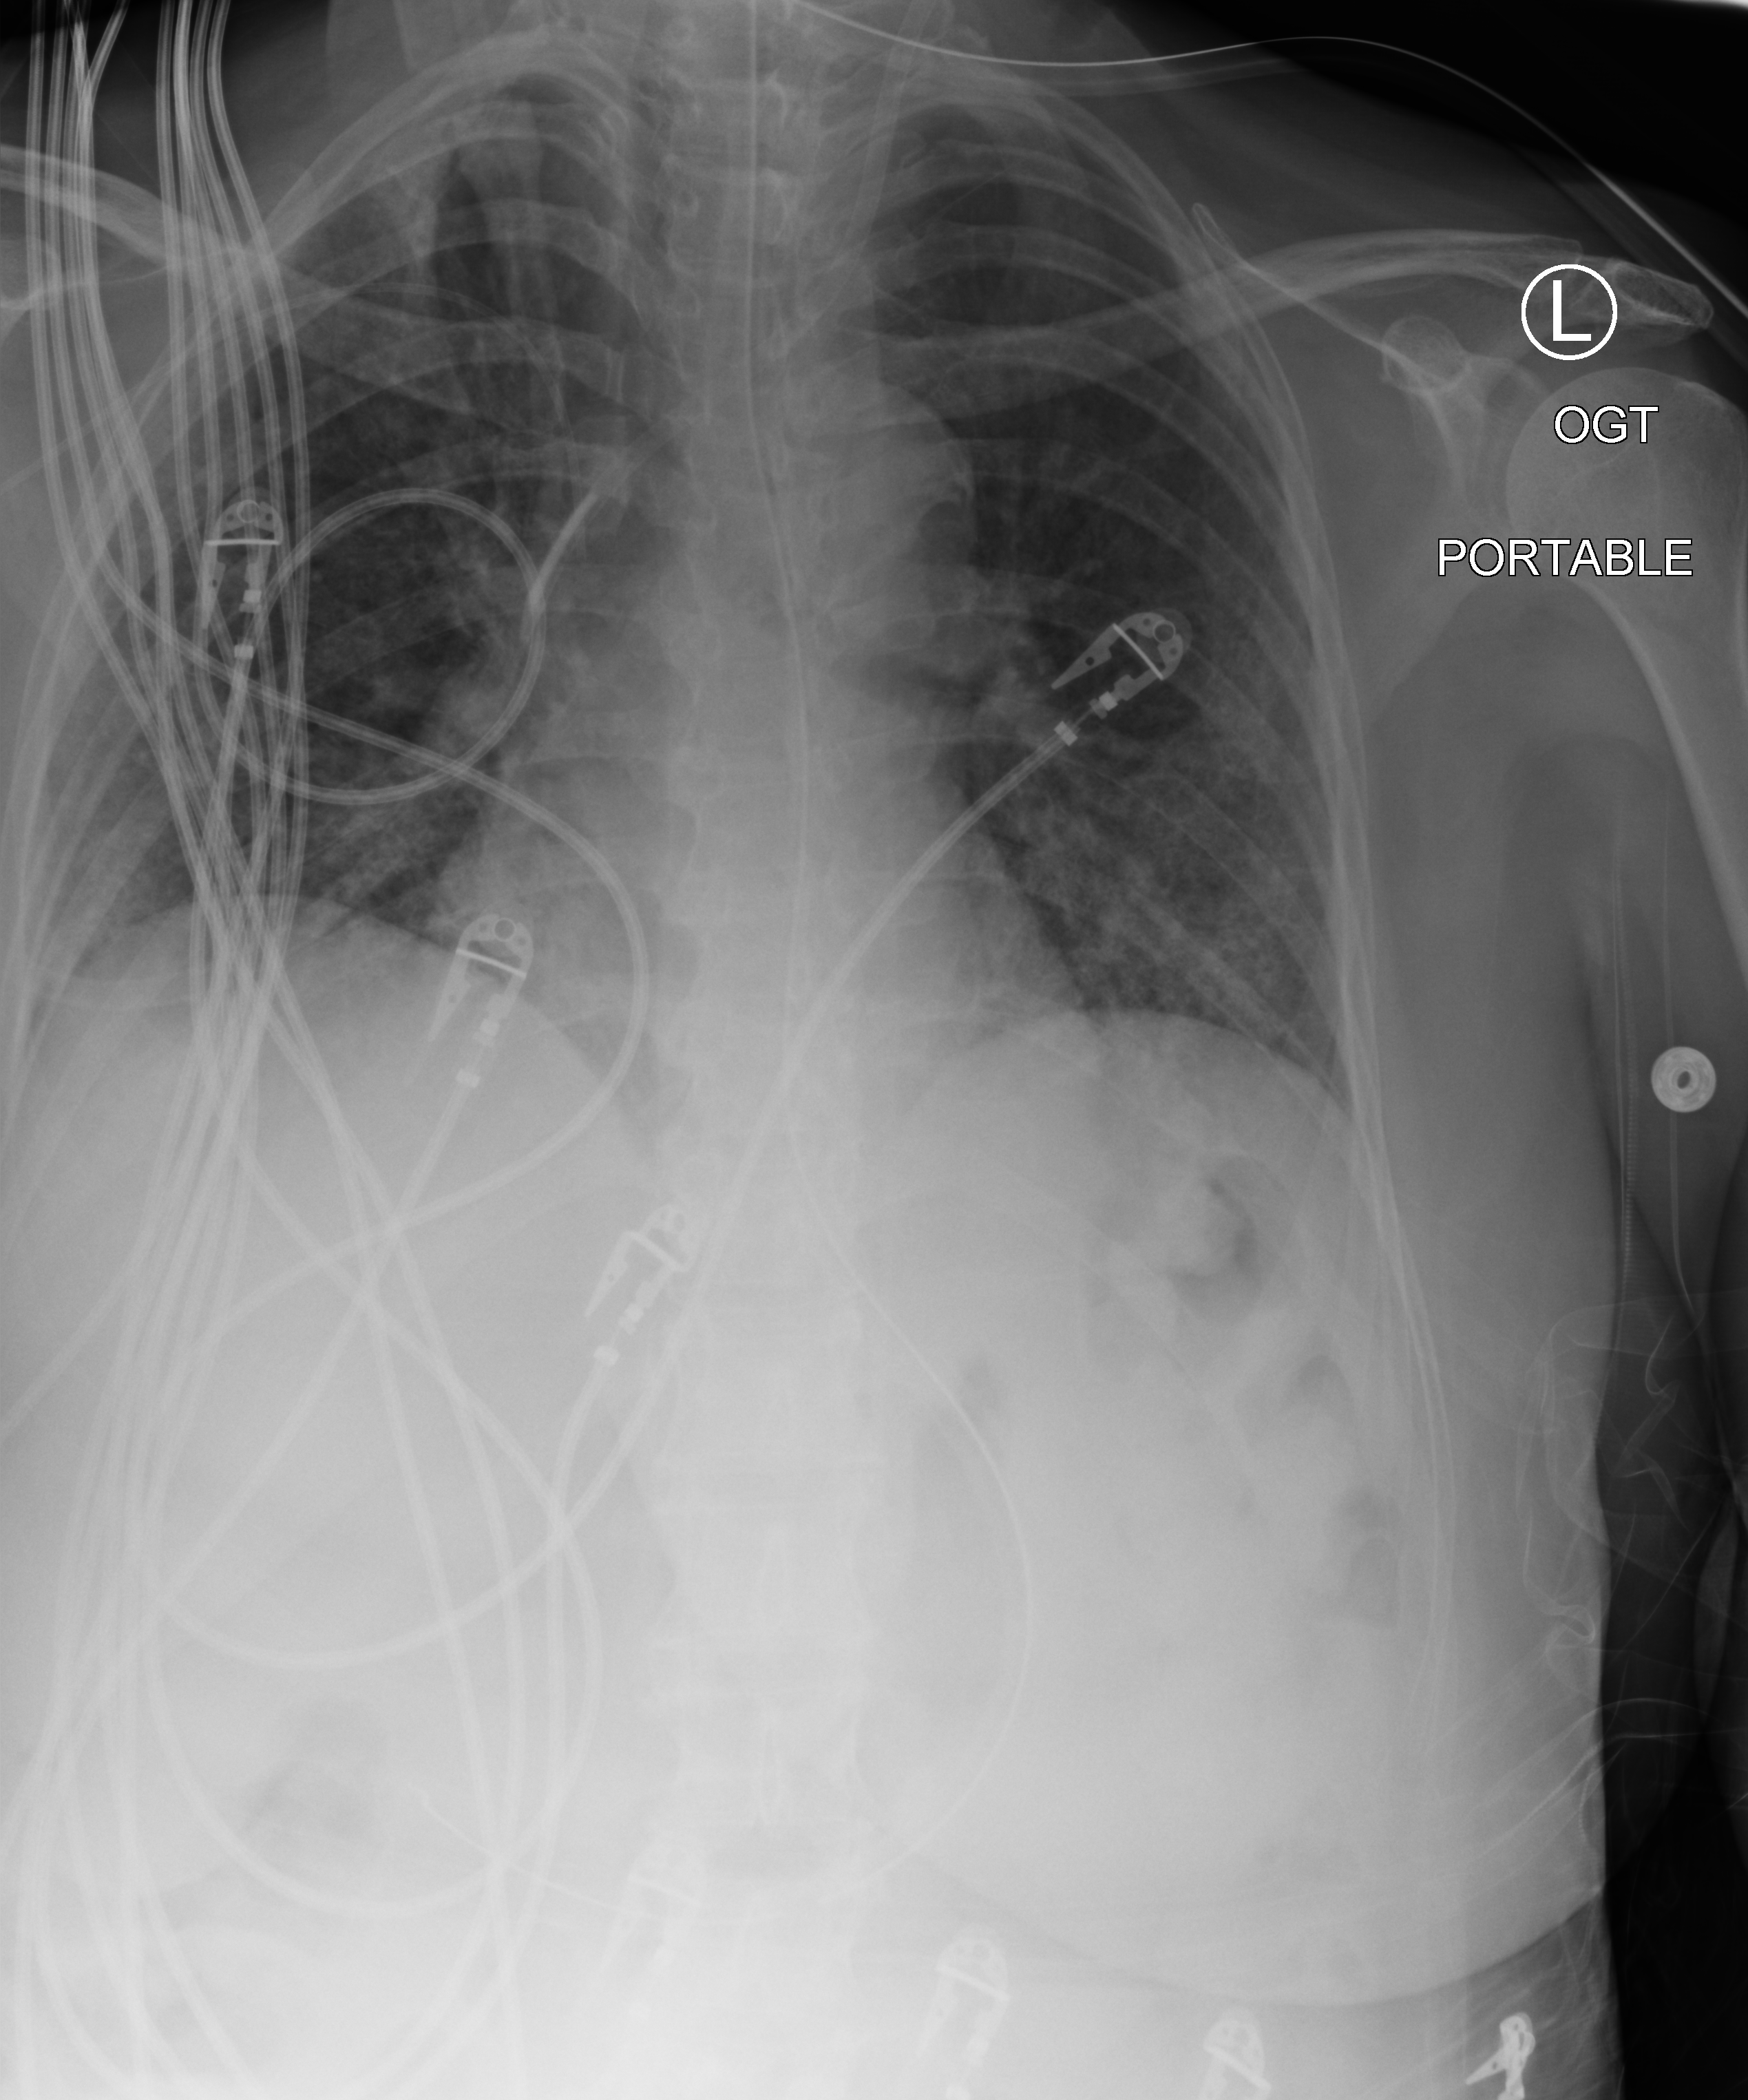
Chest X-ray (portable); anteroposterior (AP) projection. Patient hospitalised with COVID-19; female, aged 60–74 years.
Hospital-stay facts (about this admission, not read from this image; timing relative to this image not recorded): COPD (admission record): no; admitted to intensive care during this hospital stay: yes; mechanically ventilated during this hospital stay: yes.